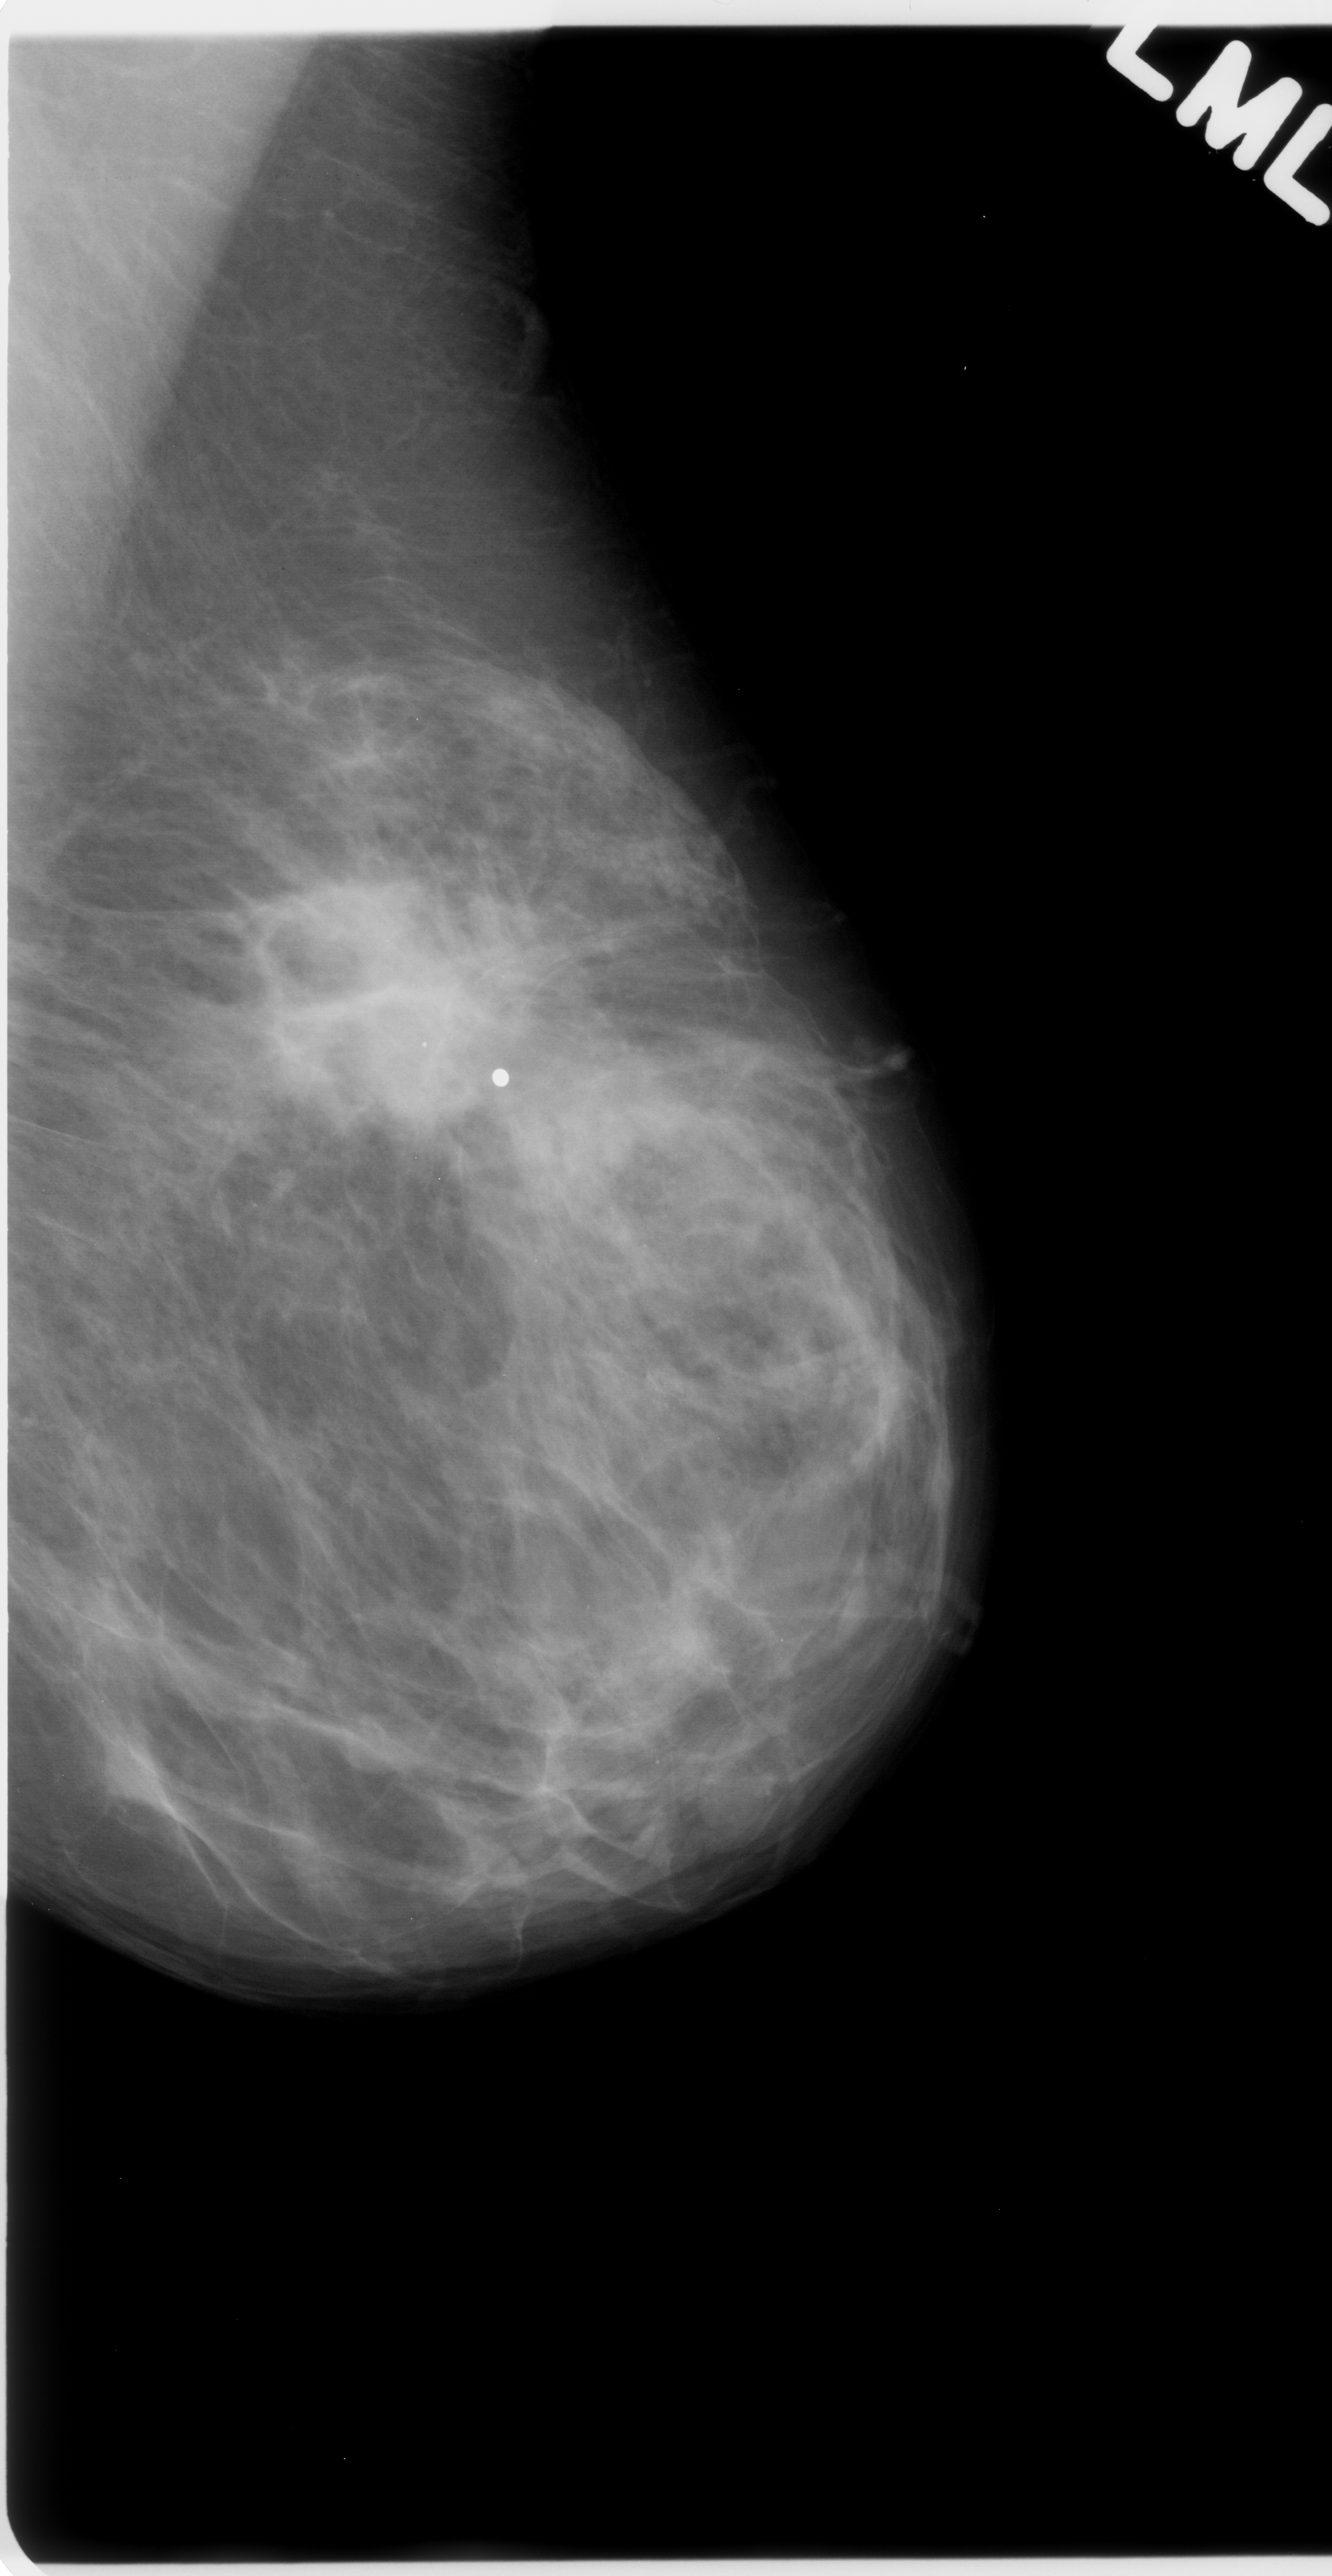
Mammogram (digitized film), left breast, MLO view, BI-RADS breast density category 2 (scale 1–4).
Marked abnormality: mass, shape irregular, margins ill defined; BI-RADS assessment category 5; pathology result (as recorded, not read from the image): malignant.